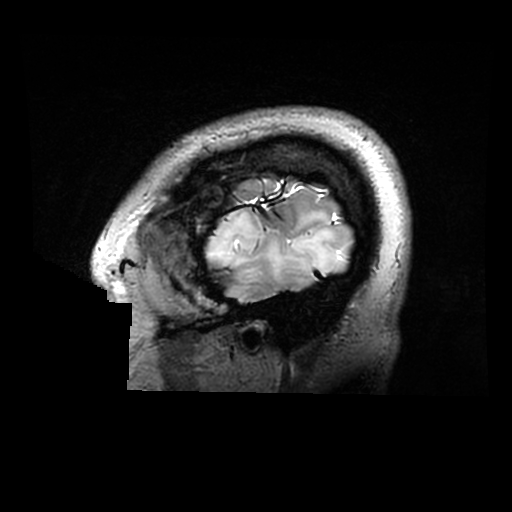
Brain MRI from a brain-tumour surgery series, one sagittal slice. Slice 253 of 320 in the series (ordered by position). 0.6 mm slice thickness. 512 × 512 image matrix, field of view 240 × 240 mm. Case-level facts recorded for this patient, not image findings: histopathology: Astrocytoma; WHO grade: 2; IDH mutation: yes.
Structures marked on this image (manually delineated by an expert):
- tumour: bounding box [x1, y1, x2, y2] px = [206, 209, 348, 284]